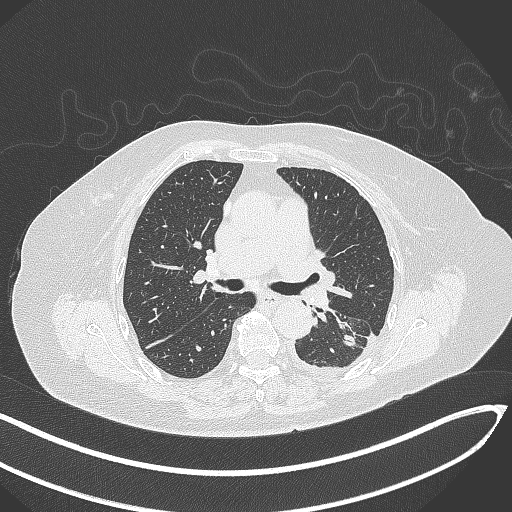
Chest CT, one axial slice; slice 190 of 270 in the series (ordered by position); lung window (W 1500 / L -600 HU); 1 mm slice thickness; 512 × 512 image matrix. Female patient, age 76 years. From the clinical record (not read from this slice): clinical TNM (as recorded): T1c N0 M0.
Structures marked on this image (rectangle marked by the reading radiologist):
- lung tumour (recorded histology: adenocarcinoma): box from (x=336, y=328) to (x=363, y=353) px